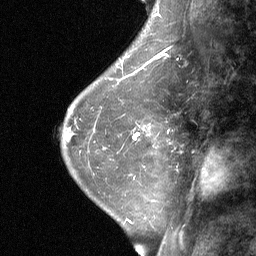
Breast MRI (dynamic contrast-enhanced), one sagittal slice. Position 19 of 64 along the scan axis. Dynamic contrast-enhanced study with each time point stored as its own series, time point 2 of 3 at this slice position (early post-contrast, ordered by acquisition time). 1.5 T. TE 4.8 ms, TR 27 ms. 2 mm slice thickness. 256 × 256 image matrix, field of view 180 × 180 mm. Female patient, age 42 years. Case-level facts recorded for this patient, not image findings: setting: breast cancer imaged before/during neoadjuvant chemotherapy; receptor status: triple-negative.
Structures marked on this image (semi-automatically segmented with operator editing):
- analysis volume of interest (the breast-tissue region the enhancement analysis was run in; not a lesion): bounding box [x1, y1, x2, y2] px = [124, 95, 176, 161]
- tumour enhancement mask (voxels above the 90 % enhancement threshold inside the analysis volume of interest): [133, 133, 139, 139]